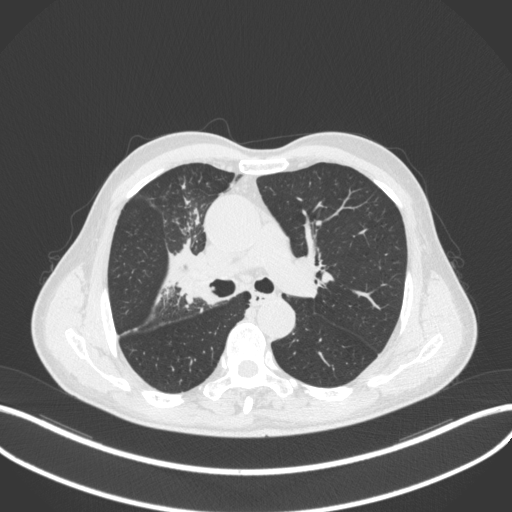
Chest CT, one axial slice. Slice 307 of 490 in the series (ordered by position). Reconstruction kernel B31f. Lung window (W 1500 / L -600 HU). 1 mm slice thickness. 512 × 512 image matrix, field of view 400 × 400 mm. Patient: male, 69 years. Case-level facts recorded for this patient, not image findings: clinical TNM (as recorded): T2a N0 M0.
Structures marked on this image (bounding box drawn by a radiologist):
- lung tumour (recorded histology: adenocarcinoma): box from (x=176, y=265) to (x=209, y=307) px